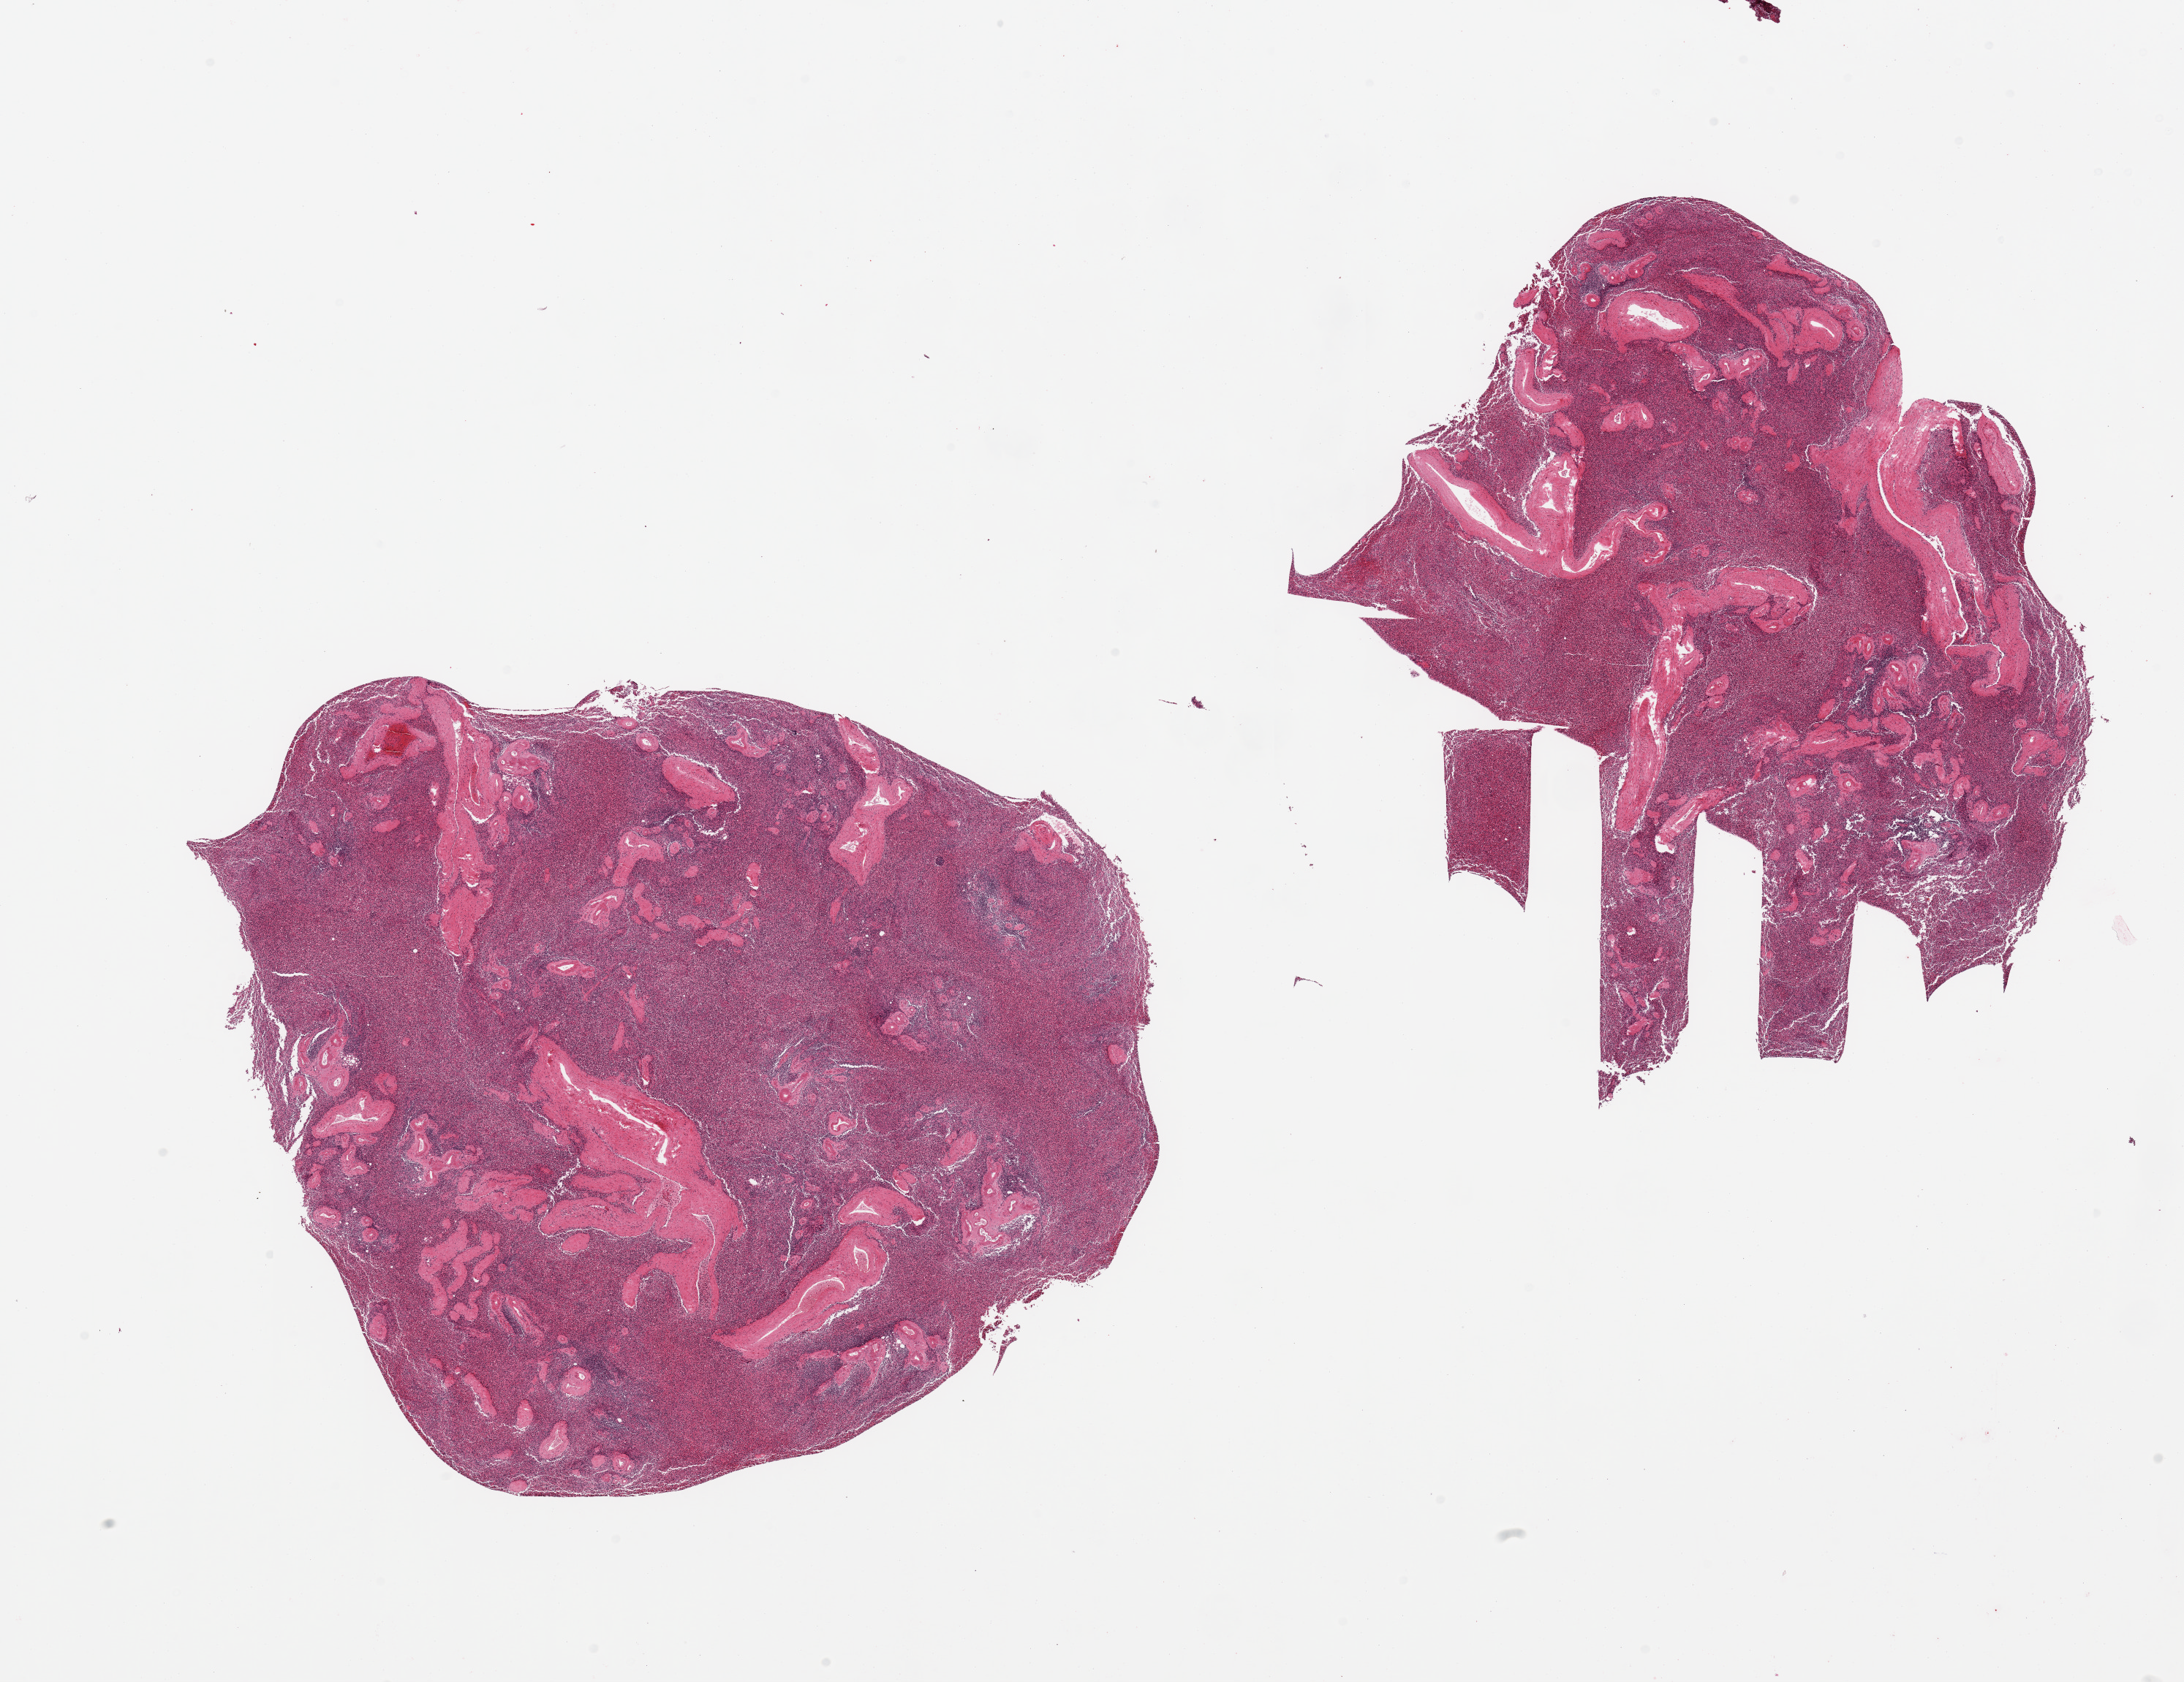
Whole-slide image, H&E stain, shown as a low-resolution overview of the whole scanned area (about 23.6 x 18.2 mm, acquisition: 20x scan), PAXgene-fixed paraffin-embedded (PFPE) section, target tissue: spleen, donor tissue sample. Donor sex: female.
Review note (as recorded): 2 pieces.